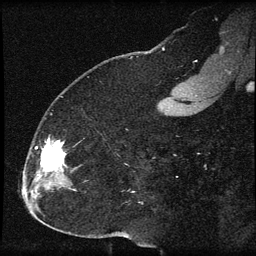
Breast MRI (dynamic contrast-enhanced), one sagittal slice; position 23 of 60 along the scan axis; dynamic contrast-enhanced series, image 2 of 3 at this slice position (ordered by acquisition); 1.5 T; TE 4.2 ms, TR 8.2 ms; 2 mm slice thickness; 256 × 256 image matrix. Patient: female, 32 years.
Outlined on this slice (semi-automatic segmentation, software-assisted and operator-edited):
- analysis volume of interest (the breast-tissue region the enhancement analysis was run in; not a lesion): bounding box (x1, y1, x2, y2) in pixels: (31, 132, 78, 184)
- tumour enhancement mask (voxels above the 70 % enhancement threshold inside the analysis volume of interest): (35, 138, 66, 176)